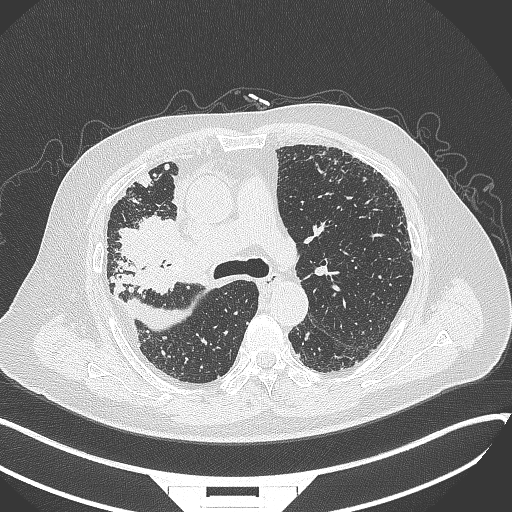
Chest CT, one axial slice. Slice 222 of 384 in the series (ordered by position). 120 kVp. Lung window (W 1500 / L -600 HU). 1 mm slice thickness. 512 × 512 image matrix. Male patient, age 69 years. From the clinical record (not read from this slice): clinical TNM (as recorded): T4 N3 M1.
Structures marked on this image (bounding box drawn by a radiologist):
- lung tumour (recorded histology: adenocarcinoma): bounding box <116,209,186,271> (left, top, right, bottom; pixels)